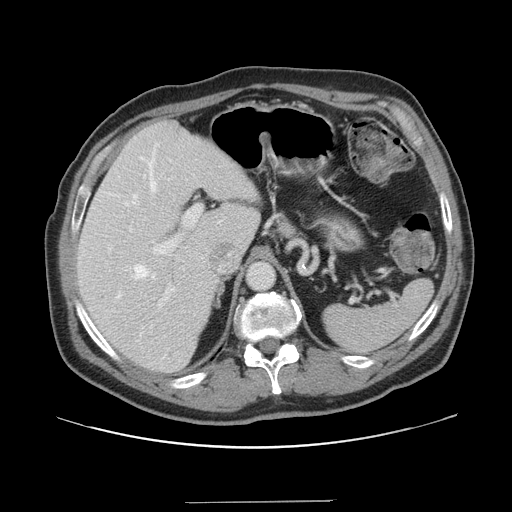
Contrast-enhanced abdominal CT, one axial slice. Slice 103 of 151 in the series (ordered by position). 120 kVp. Intravenous contrast given. Soft-tissue window (W 400 / L 40 HU). 2.5 mm slice thickness. 512 × 512 image matrix, field of view 399 × 399 mm. Male patient, age 63 years. Case-level facts recorded for this patient, not image findings: diagnosis: colorectal cancer liver metastases, imaged before liver resection.
Structures marked on this image (expert manual segmentation):
- hepatic veins: bounding box <117,144,158,329> (left, top, right, bottom; pixels)
- liver: <78,121,261,373>
- planned liver remnant (the part of the liver to remain after resection): <78,121,260,373>
- portal vein (with intrahepatic branches): <153,205,202,308>